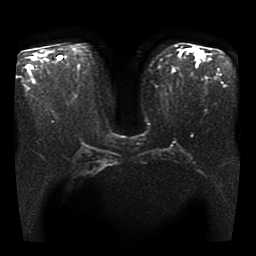
Breast MRI, one axial slice; position 19 of 40 along the scan axis; diffusion-weighted series; image 2 of 4 stored at this slice position (different b-values; order by instance number); 1.5 T; 5 mm slice thickness; 256 × 256 image matrix. Female patient.
Outlined on this slice (manually delineated by an expert):
- tumour on diffusion-weighted imaging: bounding box (x1, y1, x2, y2) in pixels: (195, 49, 200, 57)